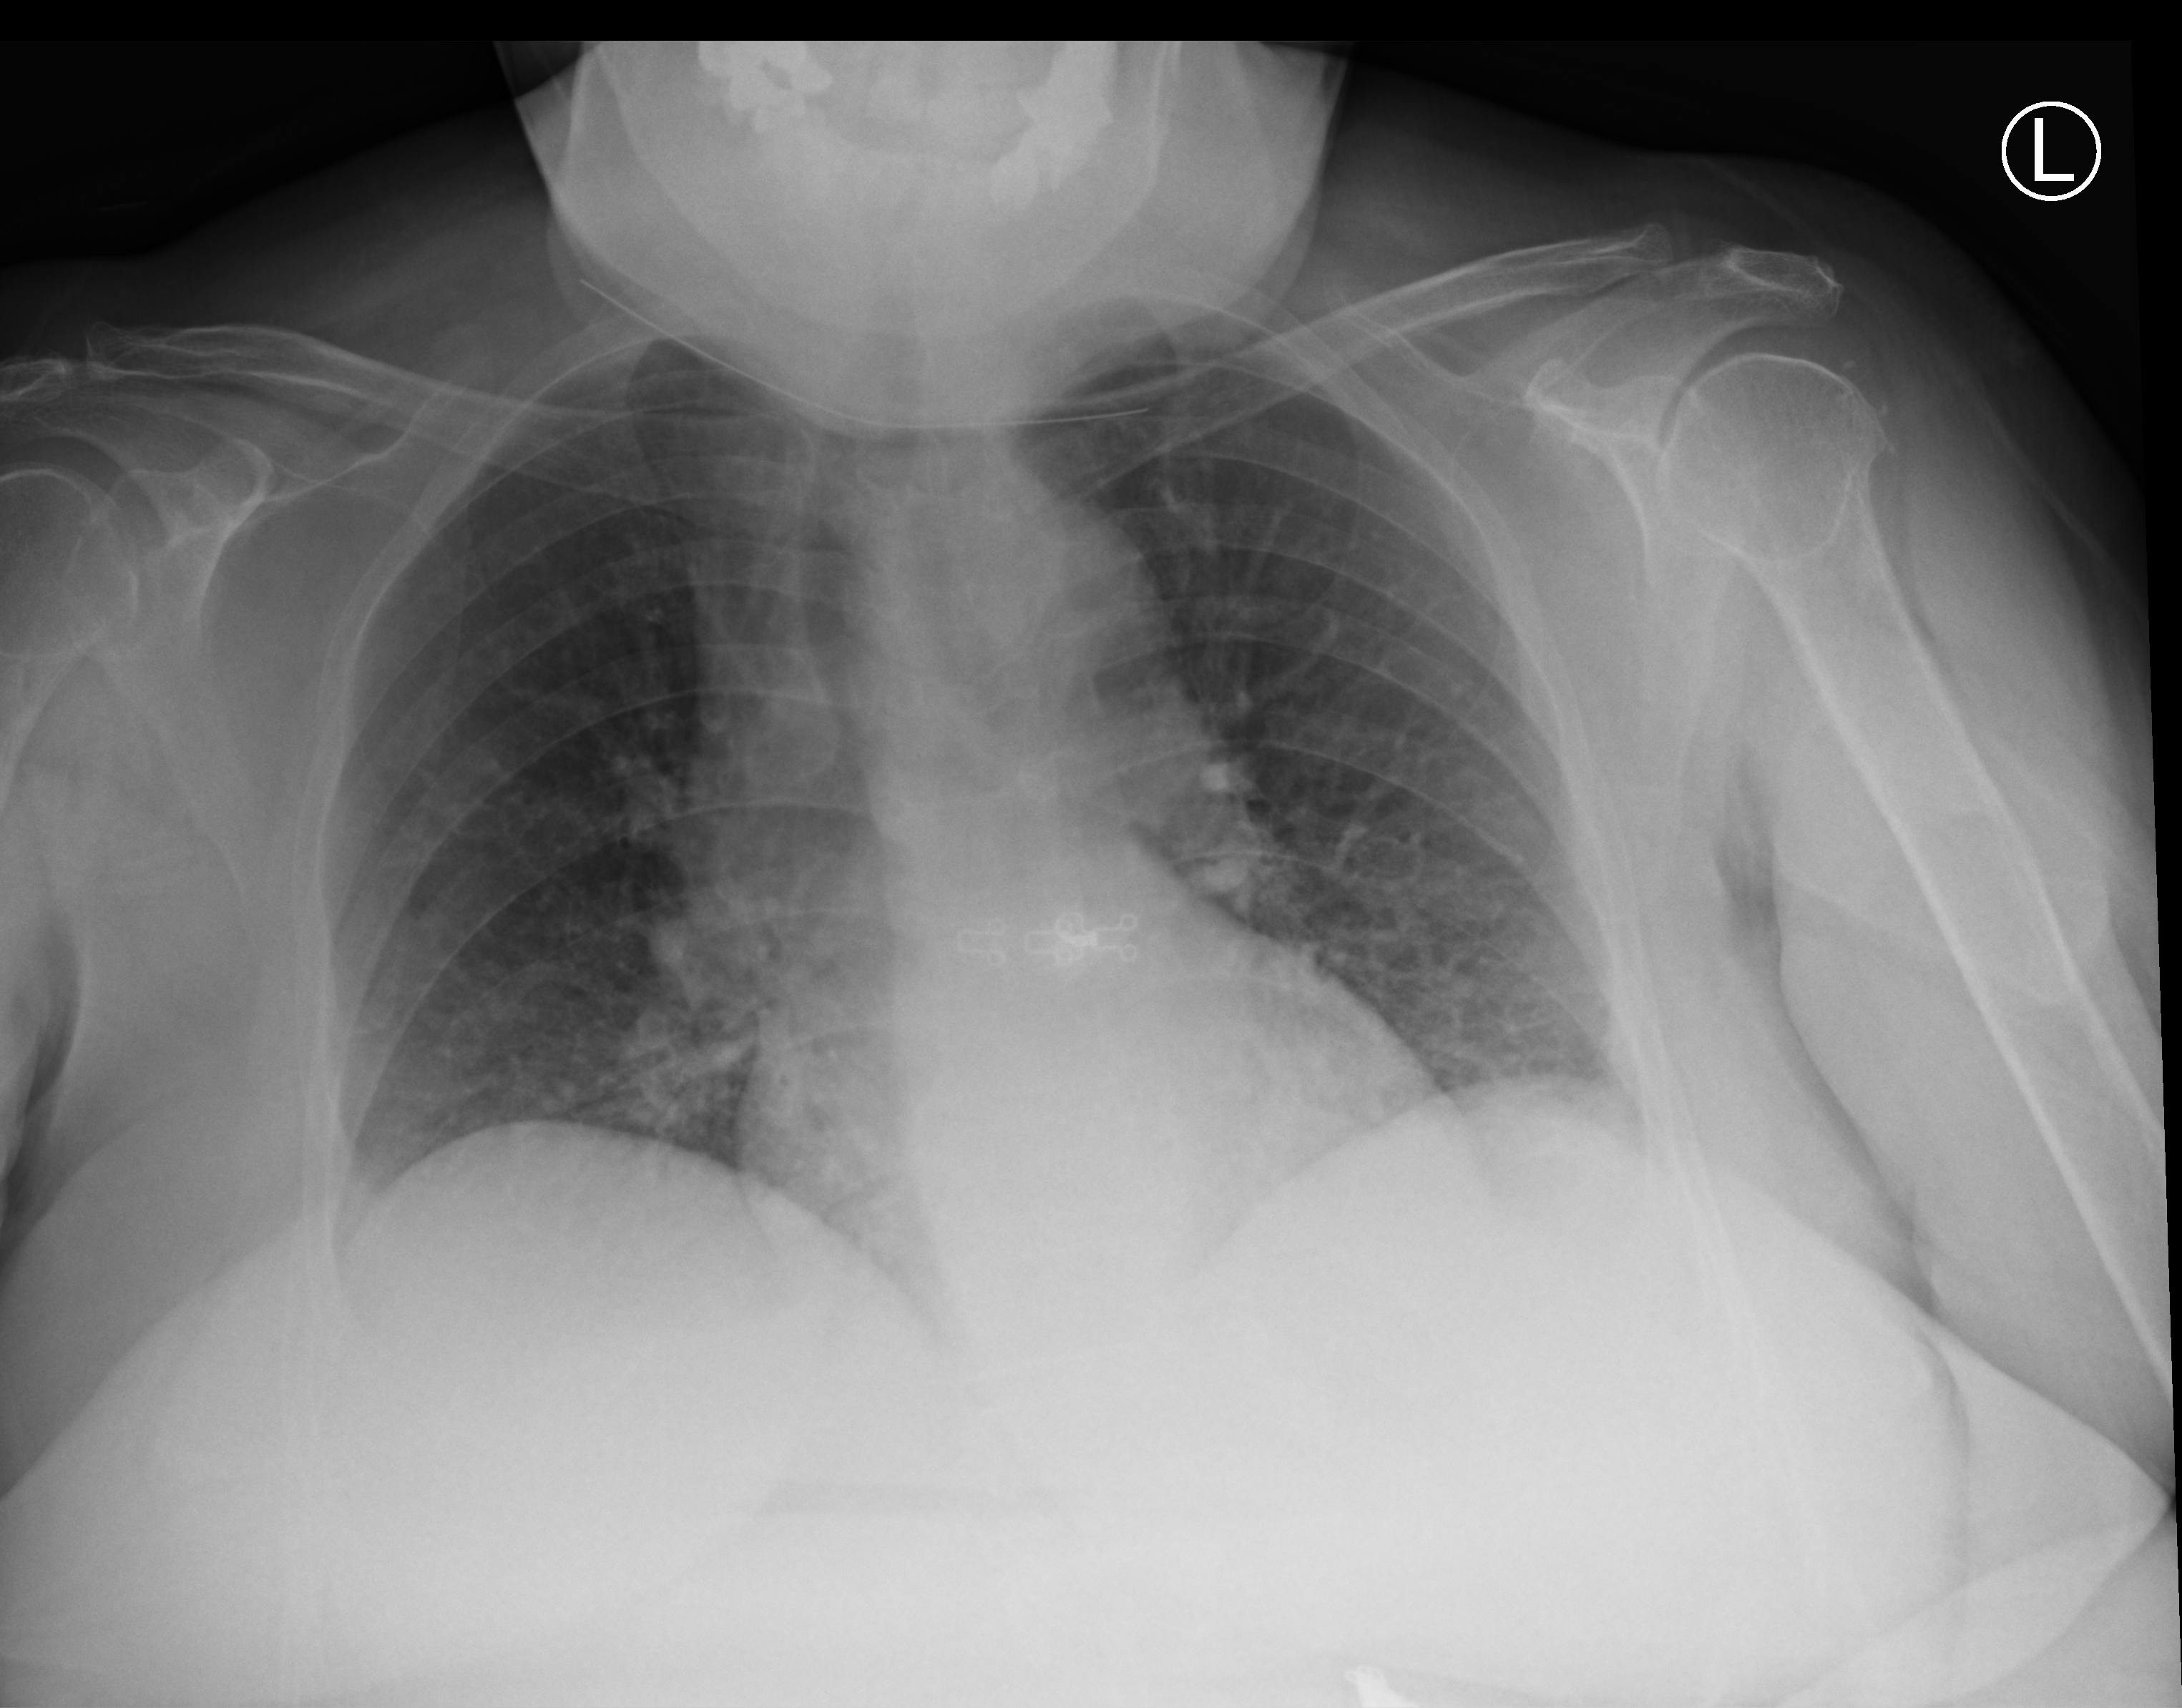
Portable chest radiograph; anteroposterior (AP) projection. Patient hospitalised with COVID-19; female, aged 60–74 years.
From the hospital-stay record, not from the radiograph (when in the stay this image was taken is not recorded):
- admitted to intensive care during this hospital stay: yes